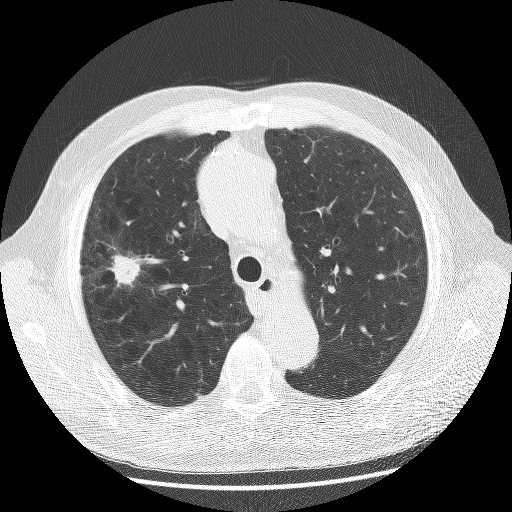
Axial slice from a low-dose chest CT screening exam. Baseline screening round. Lung window (W 1500 / L -600 HU). 2.5 mm slice thickness. Lung (sharp) reconstruction kernel (BONE). Male, age 70 years at enrolment.
• Expert reader's lesion annotation, box from (x=76, y=237) to (x=148, y=307) px.
• The screening reader recorded 2 non-calcified nodules or masses ≥4 mm on this exam; which of them this box marks is not recorded.
• Participant outcome: lung cancer diagnosed 23 days after this screen — non-small cell carcinoma, right upper lobe, poorly differentiated (G3), stage IA (AJCC 6th edition), 20 mm at pathology.